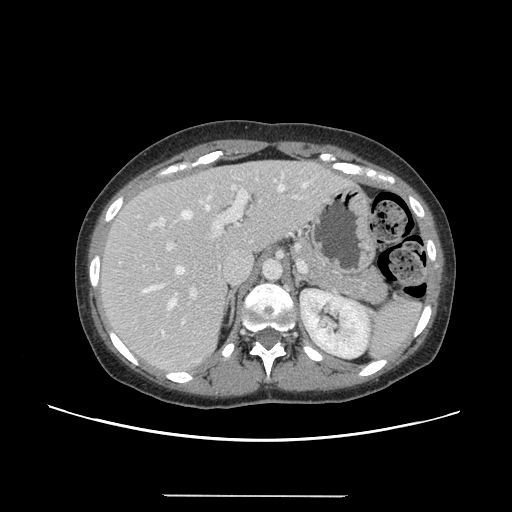
Contrast-enhanced abdominal CT, one axial slice. Position 94 of 144 along the scan axis. 120 kVp. Intravenous contrast given. Soft-tissue window (W 400 / L 40 HU). 512 × 512 image matrix, field of view 380 × 380 mm. Female patient, age 53 years. Case-level facts recorded for this patient, not image findings: diagnosis: colorectal cancer liver metastases, imaged before liver resection; multiple liver metastases: yes; largest metastasis: 1.1 cm; disease in both lobes: no.
Annotated regions visible in this slice (outlined manually by an expert reader):
- hepatic veins: bounding box [x1, y1, x2, y2] px = [142, 183, 307, 308]
- liver: [98, 161, 343, 373]
- planned liver remnant (the part of the liver to remain after resection): [97, 161, 310, 299]
- portal vein (with intrahepatic branches): [150, 179, 300, 298]